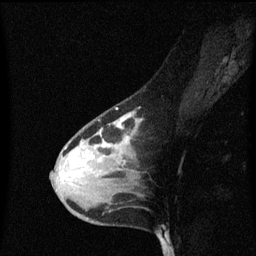
Breast MRI (dynamic contrast-enhanced), one sagittal slice; position 40 of 60 along the scan axis; dynamic contrast-enhanced series, image 2 of 3 at this slice position (ordered by acquisition); 1.5 T; TE 4.2 ms, TR 8.4 ms; 2 mm slice thickness; 256 × 256 image matrix, field of view 200 × 200 mm. Female patient, age 38 years. From the clinical record (not read from this slice): setting: breast cancer imaged before/during neoadjuvant chemotherapy; receptor status: HR-positive, HER2-negative.
Annotated regions visible in this slice (semi-automatically segmented with operator editing):
- analysis volume of interest (the breast-tissue region the enhancement analysis was run in; not a lesion): bounding box [x1, y1, x2, y2] px = [52, 104, 141, 205]
- tumour enhancement mask (voxels above the 70 % enhancement threshold inside the analysis volume of interest): [64, 112, 141, 177]